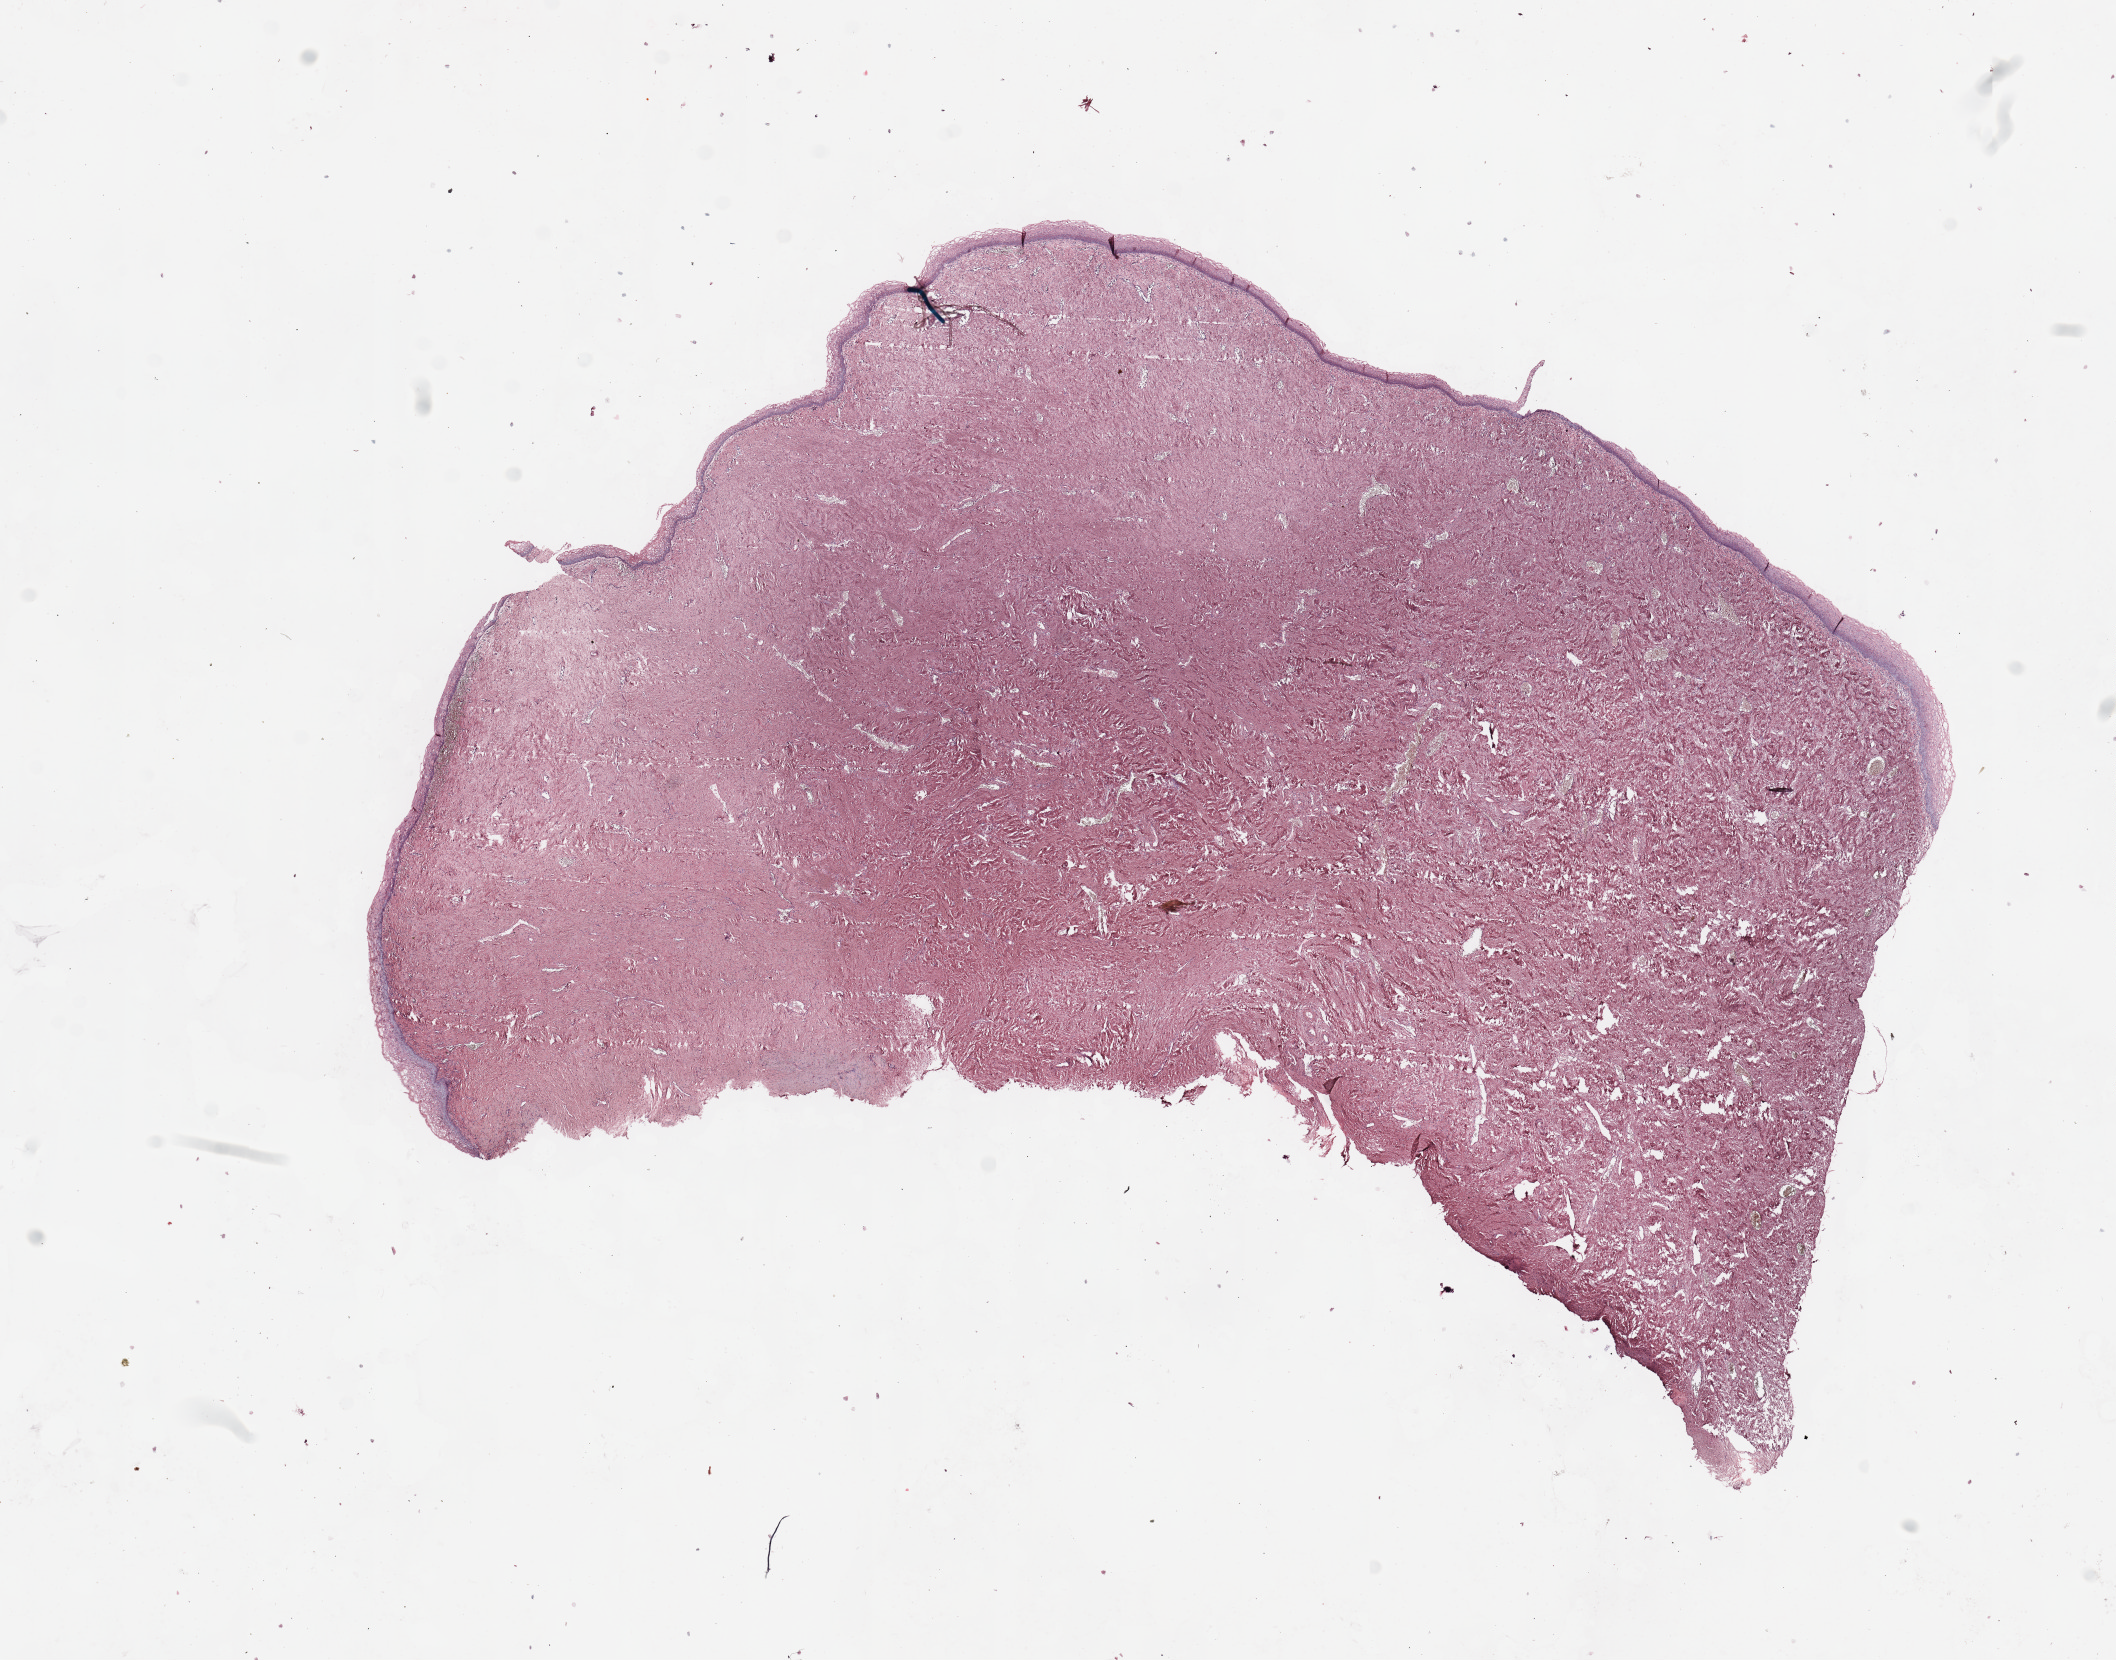
Whole-slide histology image, H&E-stained, whole scanned area (about 16.7 x 13.1 mm, acquisition: 20x scan) shown as a low-resolution overview; uterus, normal (non-tumour) tissue. Female, 68 y/o.
This section: normal (non-tumour) tissue from the same patient. Patient diagnosis: Endometrioid adenocarcinoma, NOS.